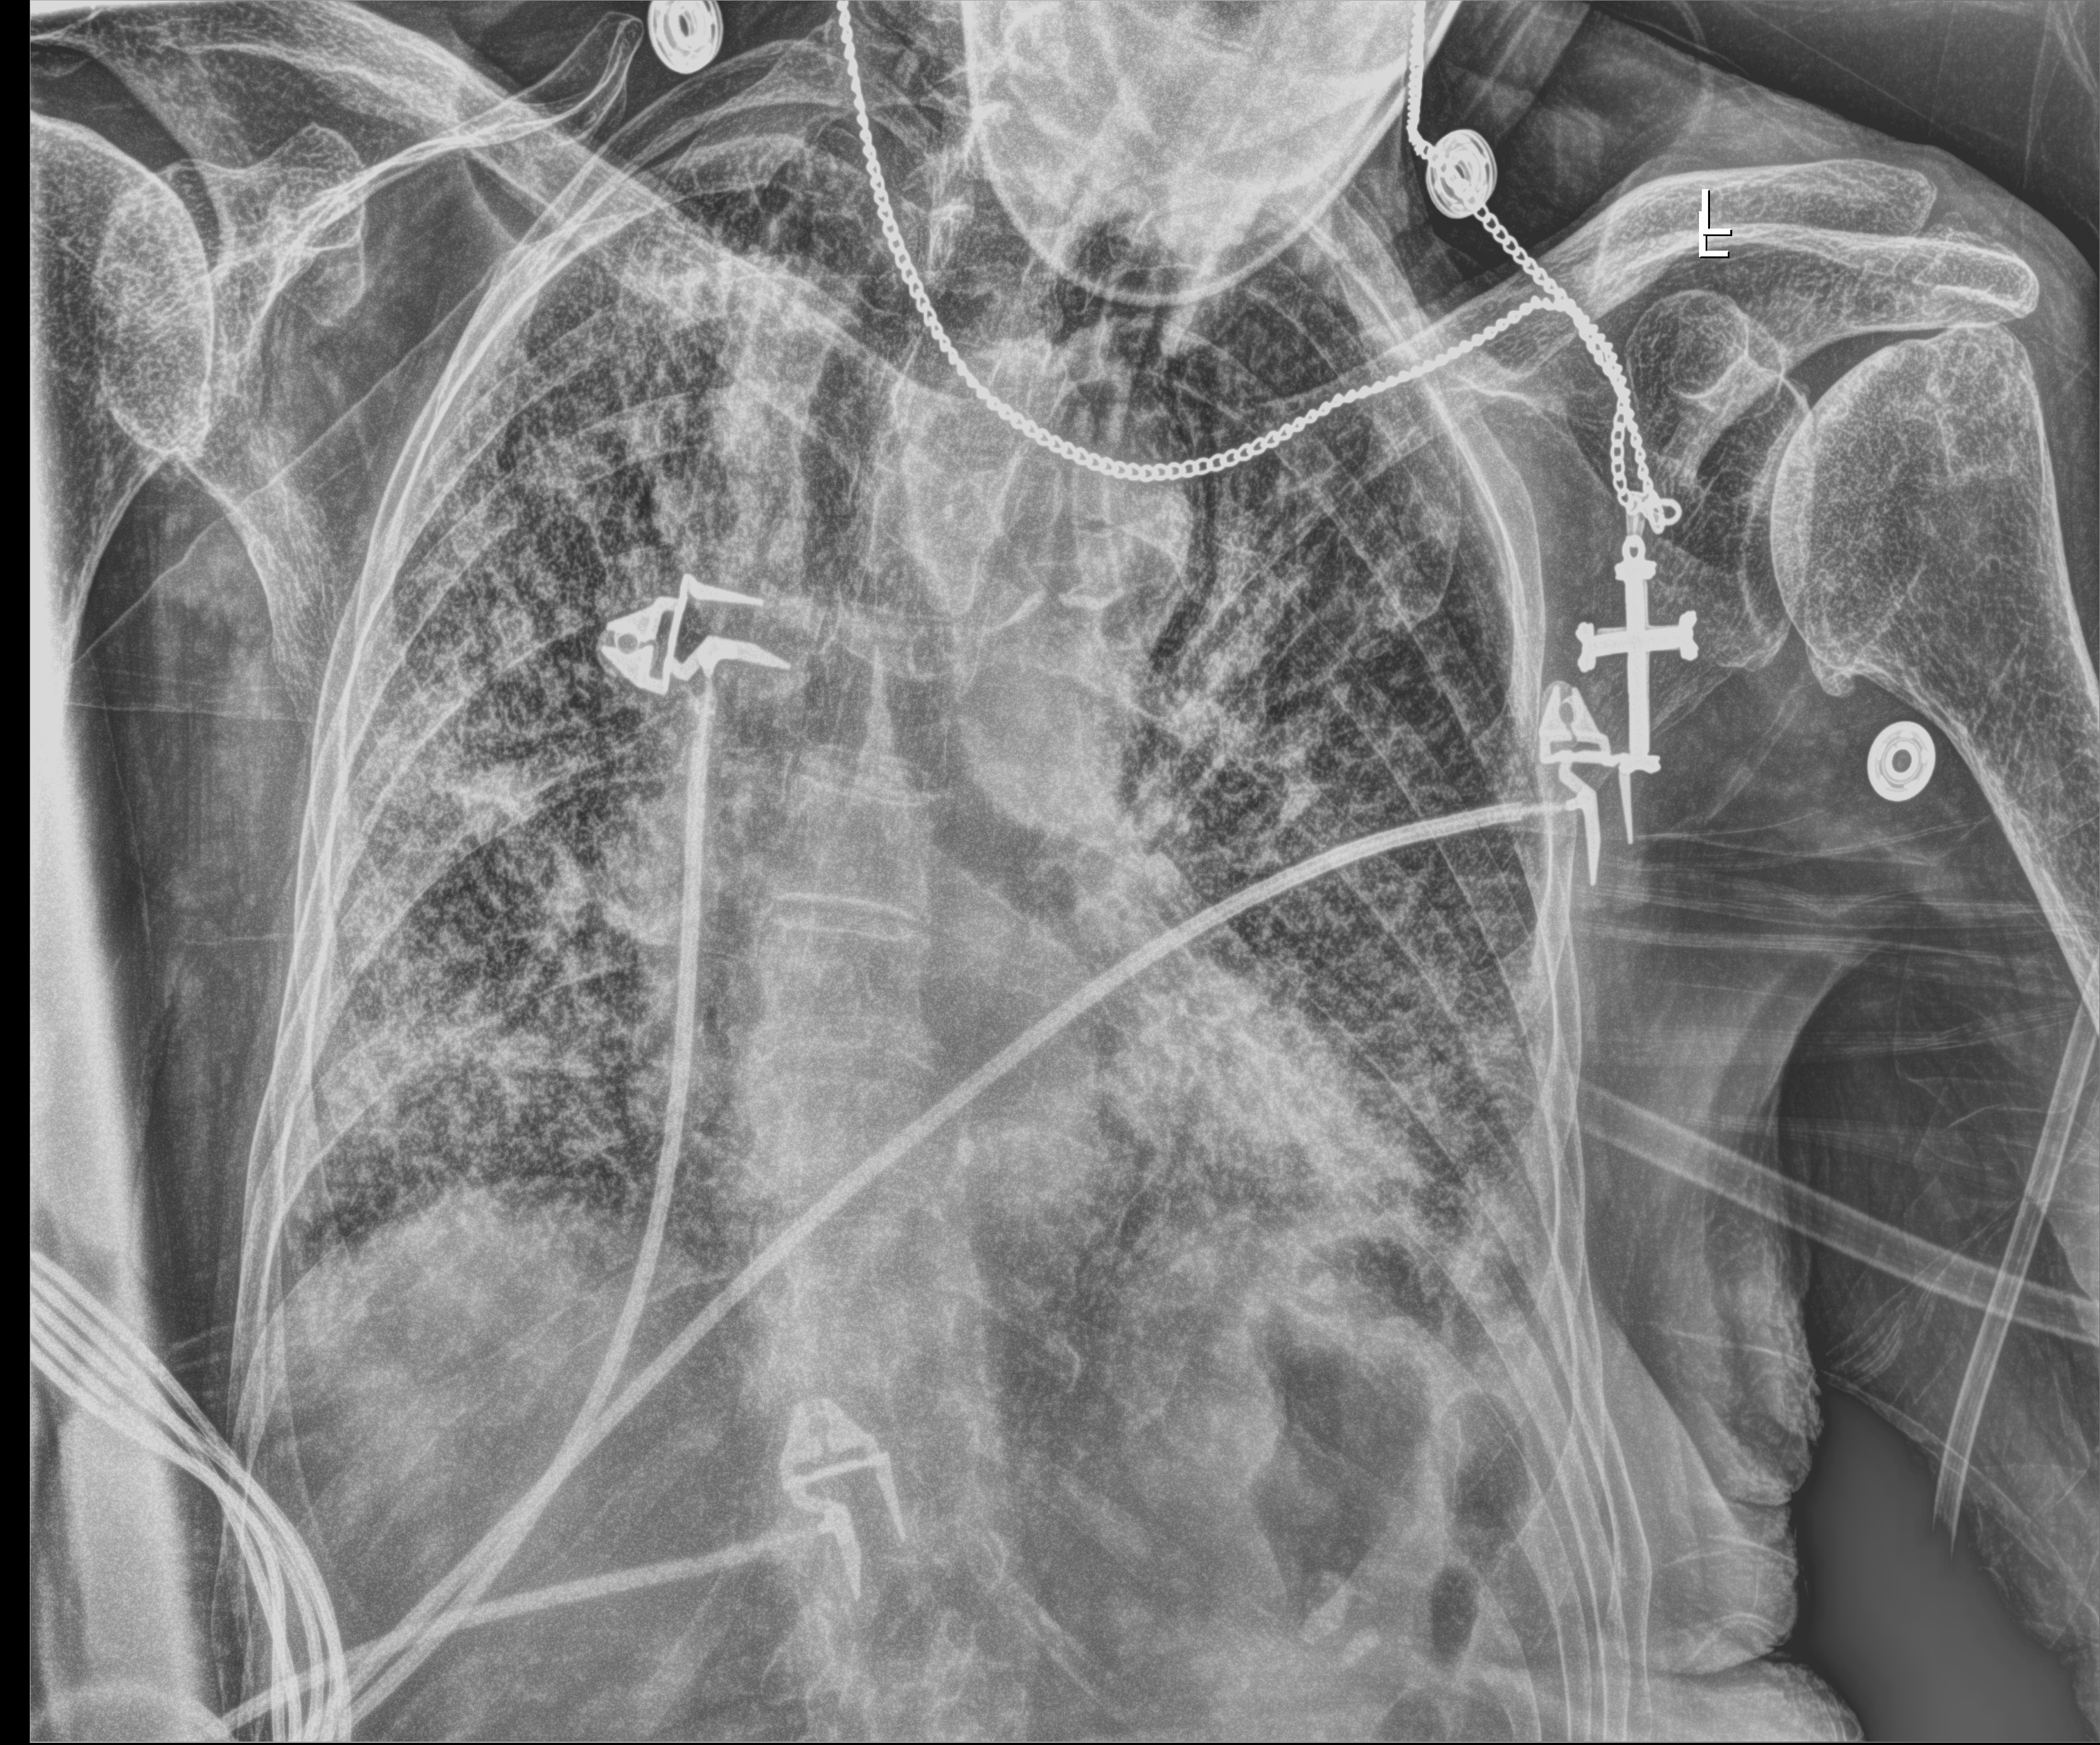
Bedside chest radiograph (digital radiography). Patient hospitalised with COVID-19; female, aged 75–90 years.
Hospital-stay facts (about this admission, not read from this image; timing relative to this image not recorded):
- length of hospital stay: 11 days
- mechanically ventilated during this hospital stay: no